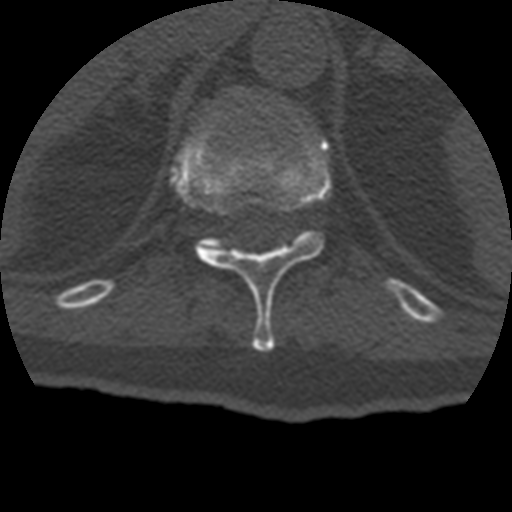
CT including the spine, one axial slice. Position 190 of 399 along the scan axis. Reconstruction kernel STANDARD. 120 kVp. Bone window (W 1800 / L 400 HU). 1.25 mm slice thickness. 512 × 512 image matrix. Patient age 69 years. From the clinical record (not read from this slice): primary cancer: prostate.
Outlined on this slice (semi-automatically segmented with operator editing):
- T11 vertebra: bounding box (x1, y1, x2, y2) in pixels: (172, 120, 331, 351)
- T12 vertebra: (225, 245, 231, 250)